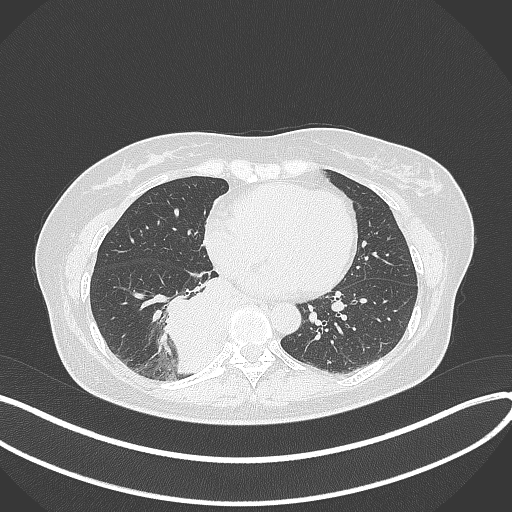
Chest CT, one axial slice. Position 135 of 331 along the scan axis. Lung window (W 1500 / L -600 HU). 1 mm slice thickness. 512 × 512 image matrix. Female patient, age 54 years. Case-level facts recorded for this patient, not image findings: clinical TNM (as recorded): T4 N0 M0.
Annotated regions visible in this slice (rectangle marked by the reading radiologist):
- lung tumour (recorded histology: adenocarcinoma): bounding box <169,272,238,375> (left, top, right, bottom; pixels)